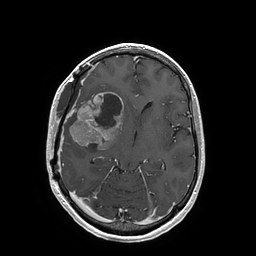
Brain MRI from a brain-tumour surgery series, one axial slice. T1-weighted post-contrast. 256 × 256 image matrix. From the clinical record (not read from this slice): histopathology: Glioblastoma; WHO grade: 4; IDH mutation: no.
Annotated regions visible in this slice (manually delineated by an expert):
- tumour: bounding box <69,92,123,150> (left, top, right, bottom; pixels)